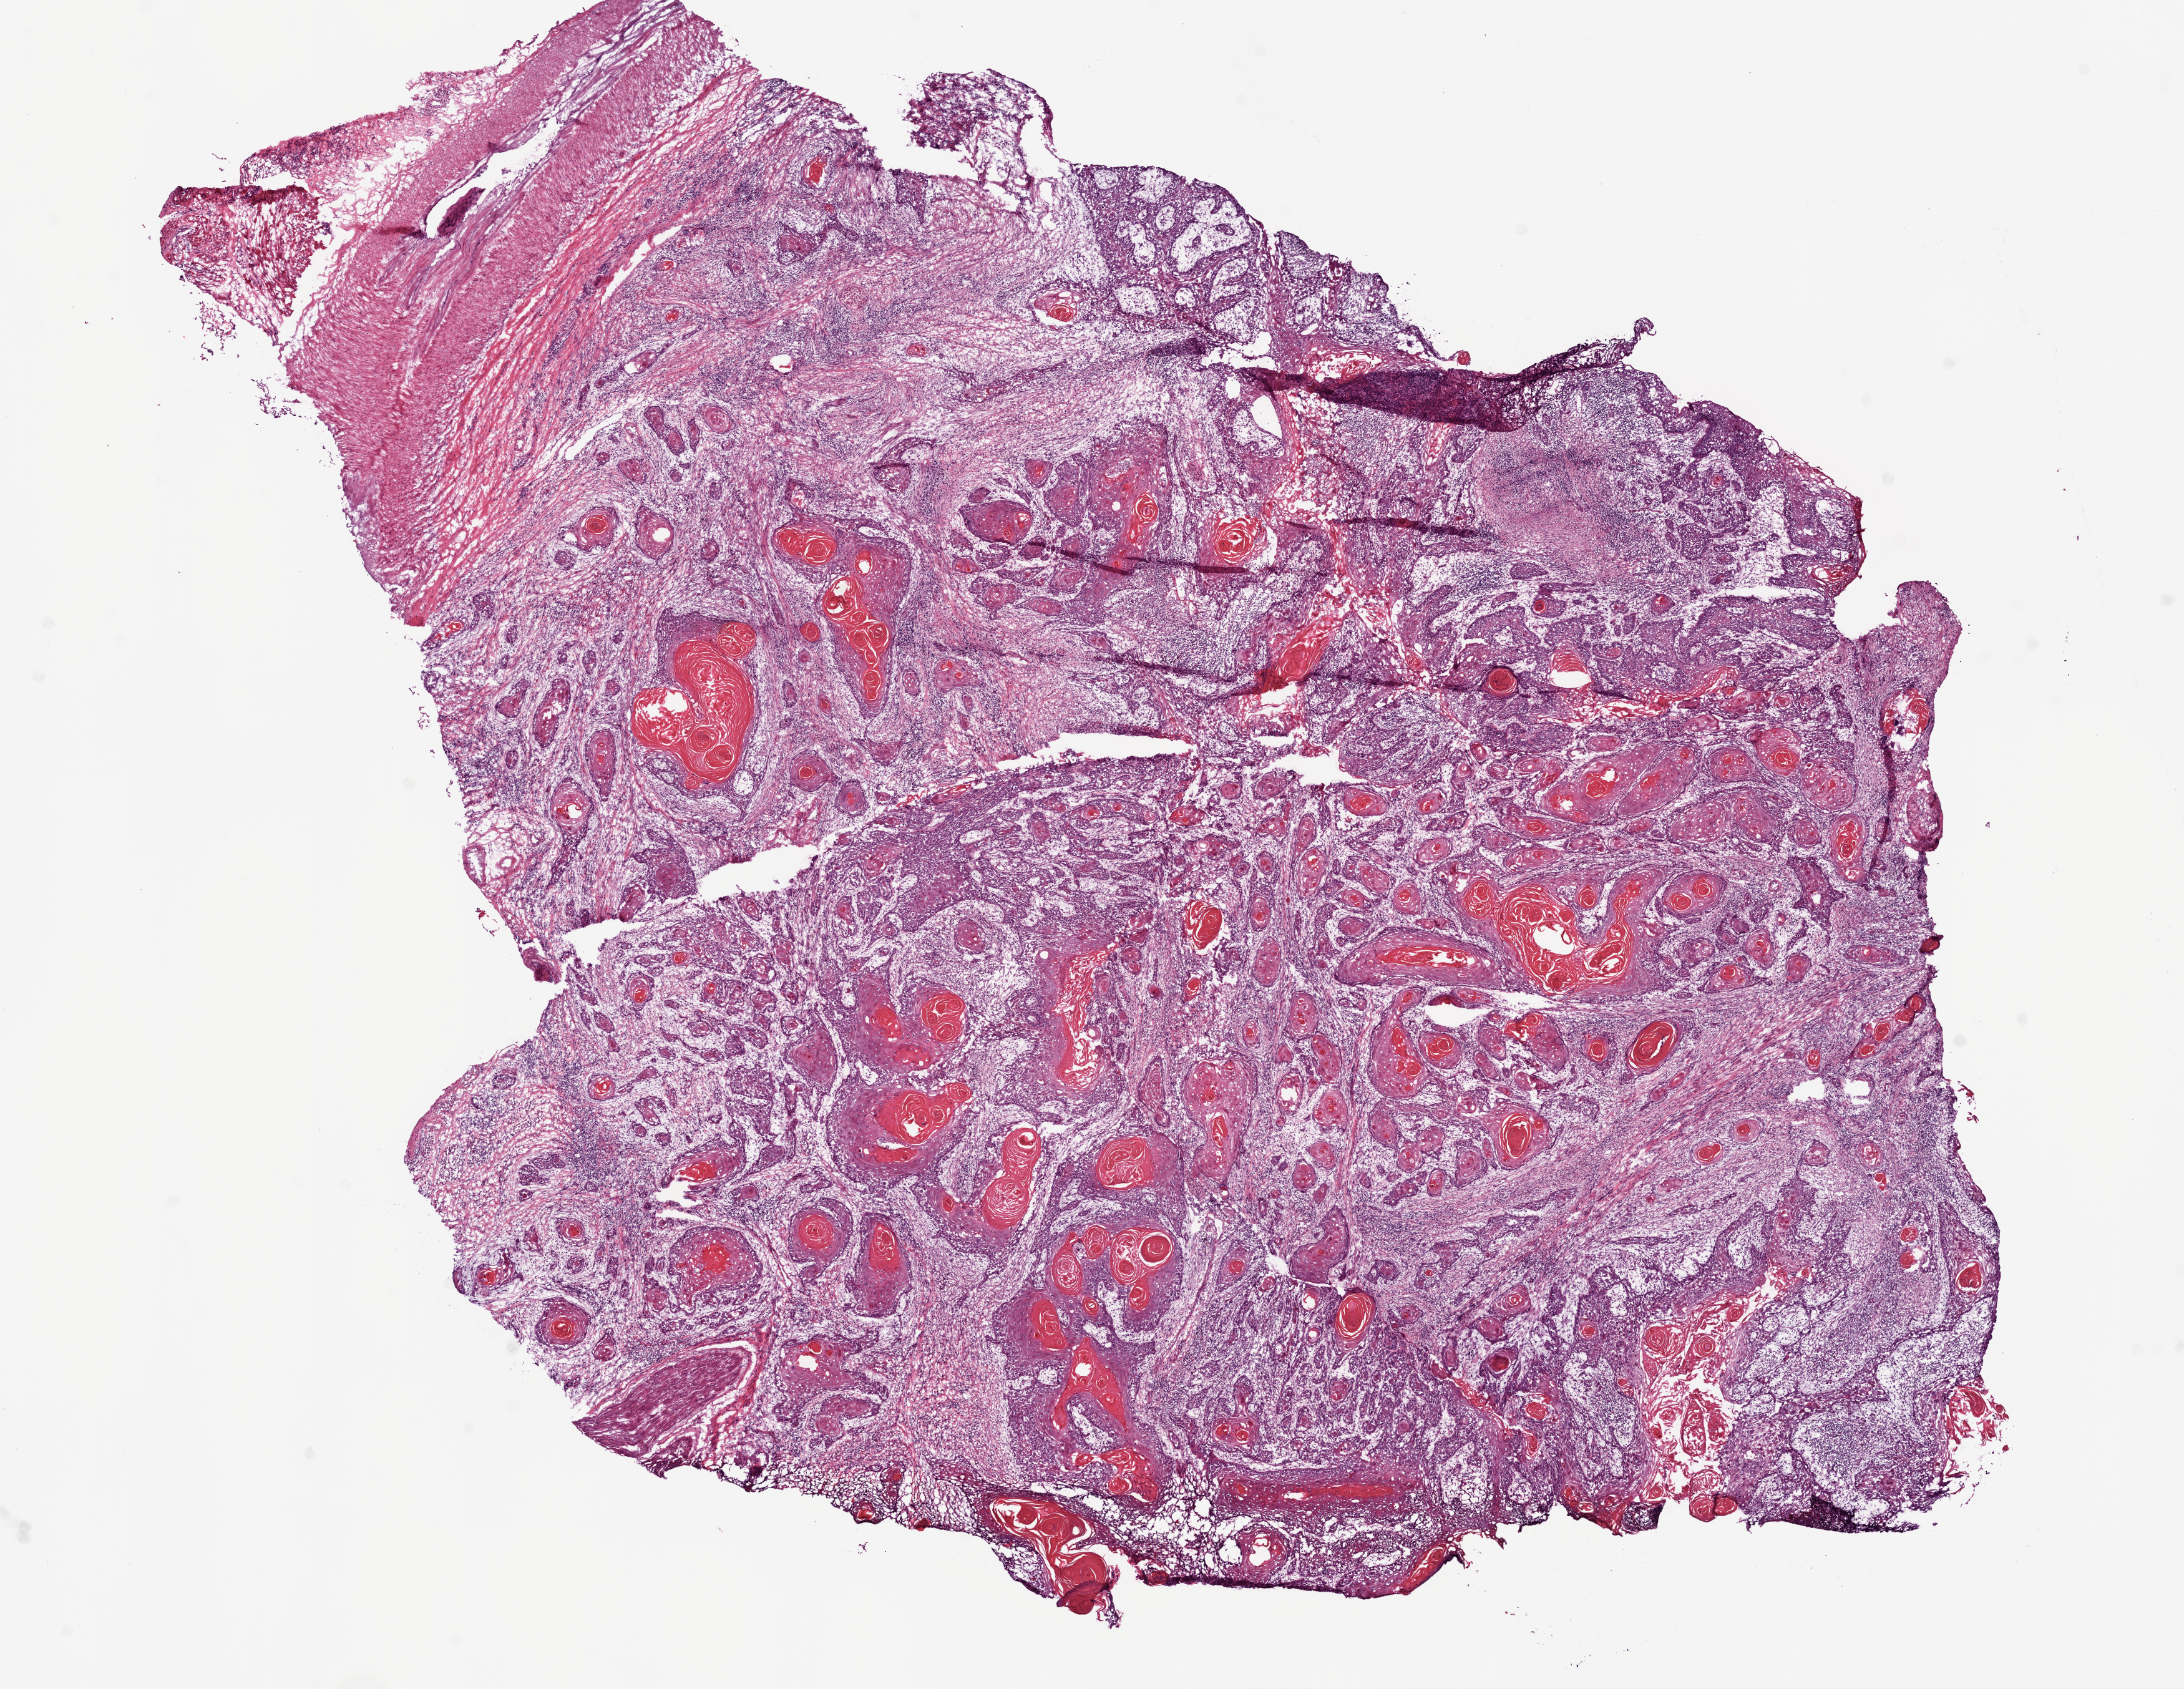
H&E-stained whole-slide image — low-resolution overview of the scanned area, about 14.0 x 10.9 mm (slide scanned at 20x). Frozen section from the bottom of the tissue portion. Head and neck, primary tumour sample. Female, age 48 years at initial diagnosis. Histologic grade: G3 (poorly differentiated). Pathologist review of this section (percent, as recorded): tumour cells 90%, tumour nuclei 70%, normal cells 5%, stromal cells 3%, necrosis 2%. Inflammatory infiltration, as recorded: lymphocyte infiltration 25%, neutrophil infiltration 5%.
Pathologic diagnosis: Squamous cell carcinoma, NOS (tongue, NOS). TNM: T4a N2b M0. AJCC pathologic stage: IVA.